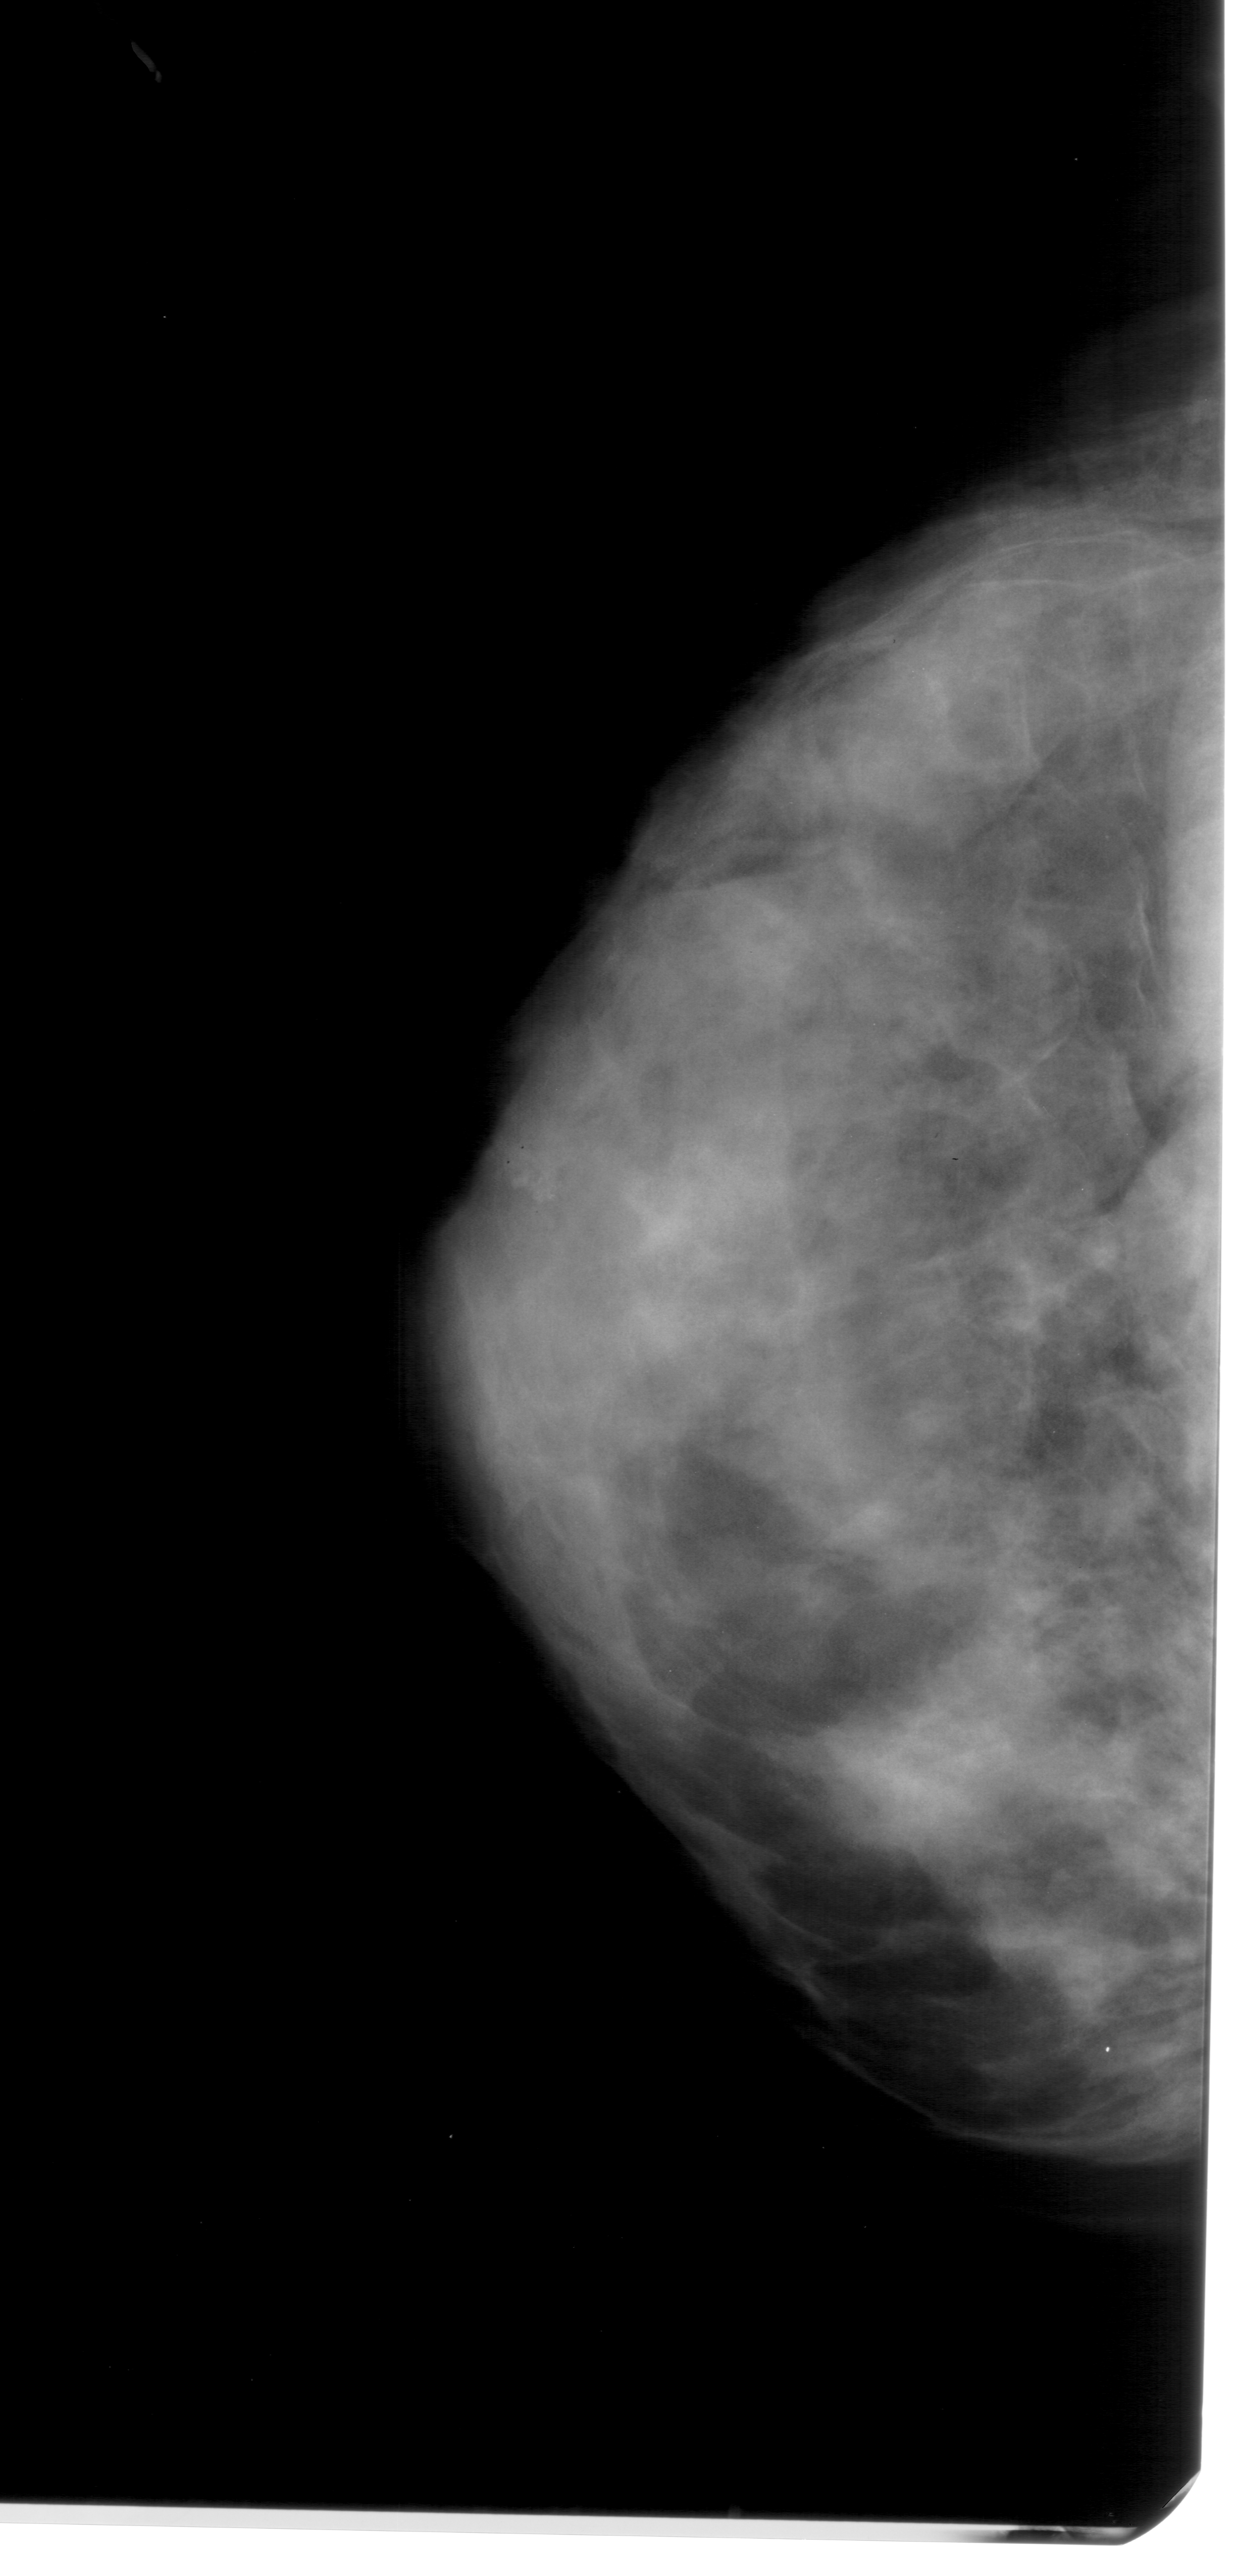
Scanned film-screen mammogram. Left breast. CC view. BI-RADS breast density category 4 (scale 1–4). 1235 × 2576 image matrix.
Marked abnormalities (boxes around the expert regions of interest):
- calcifications, morphology pleomorphic, distribution clustered; BI-RADS assessment category 4; subtlety rating 2 on a 1 (subtle) to 5 (obvious) scale; pathology result (as recorded, not read from the image): benign: box from (x=502, y=1142) to (x=585, y=1224) px